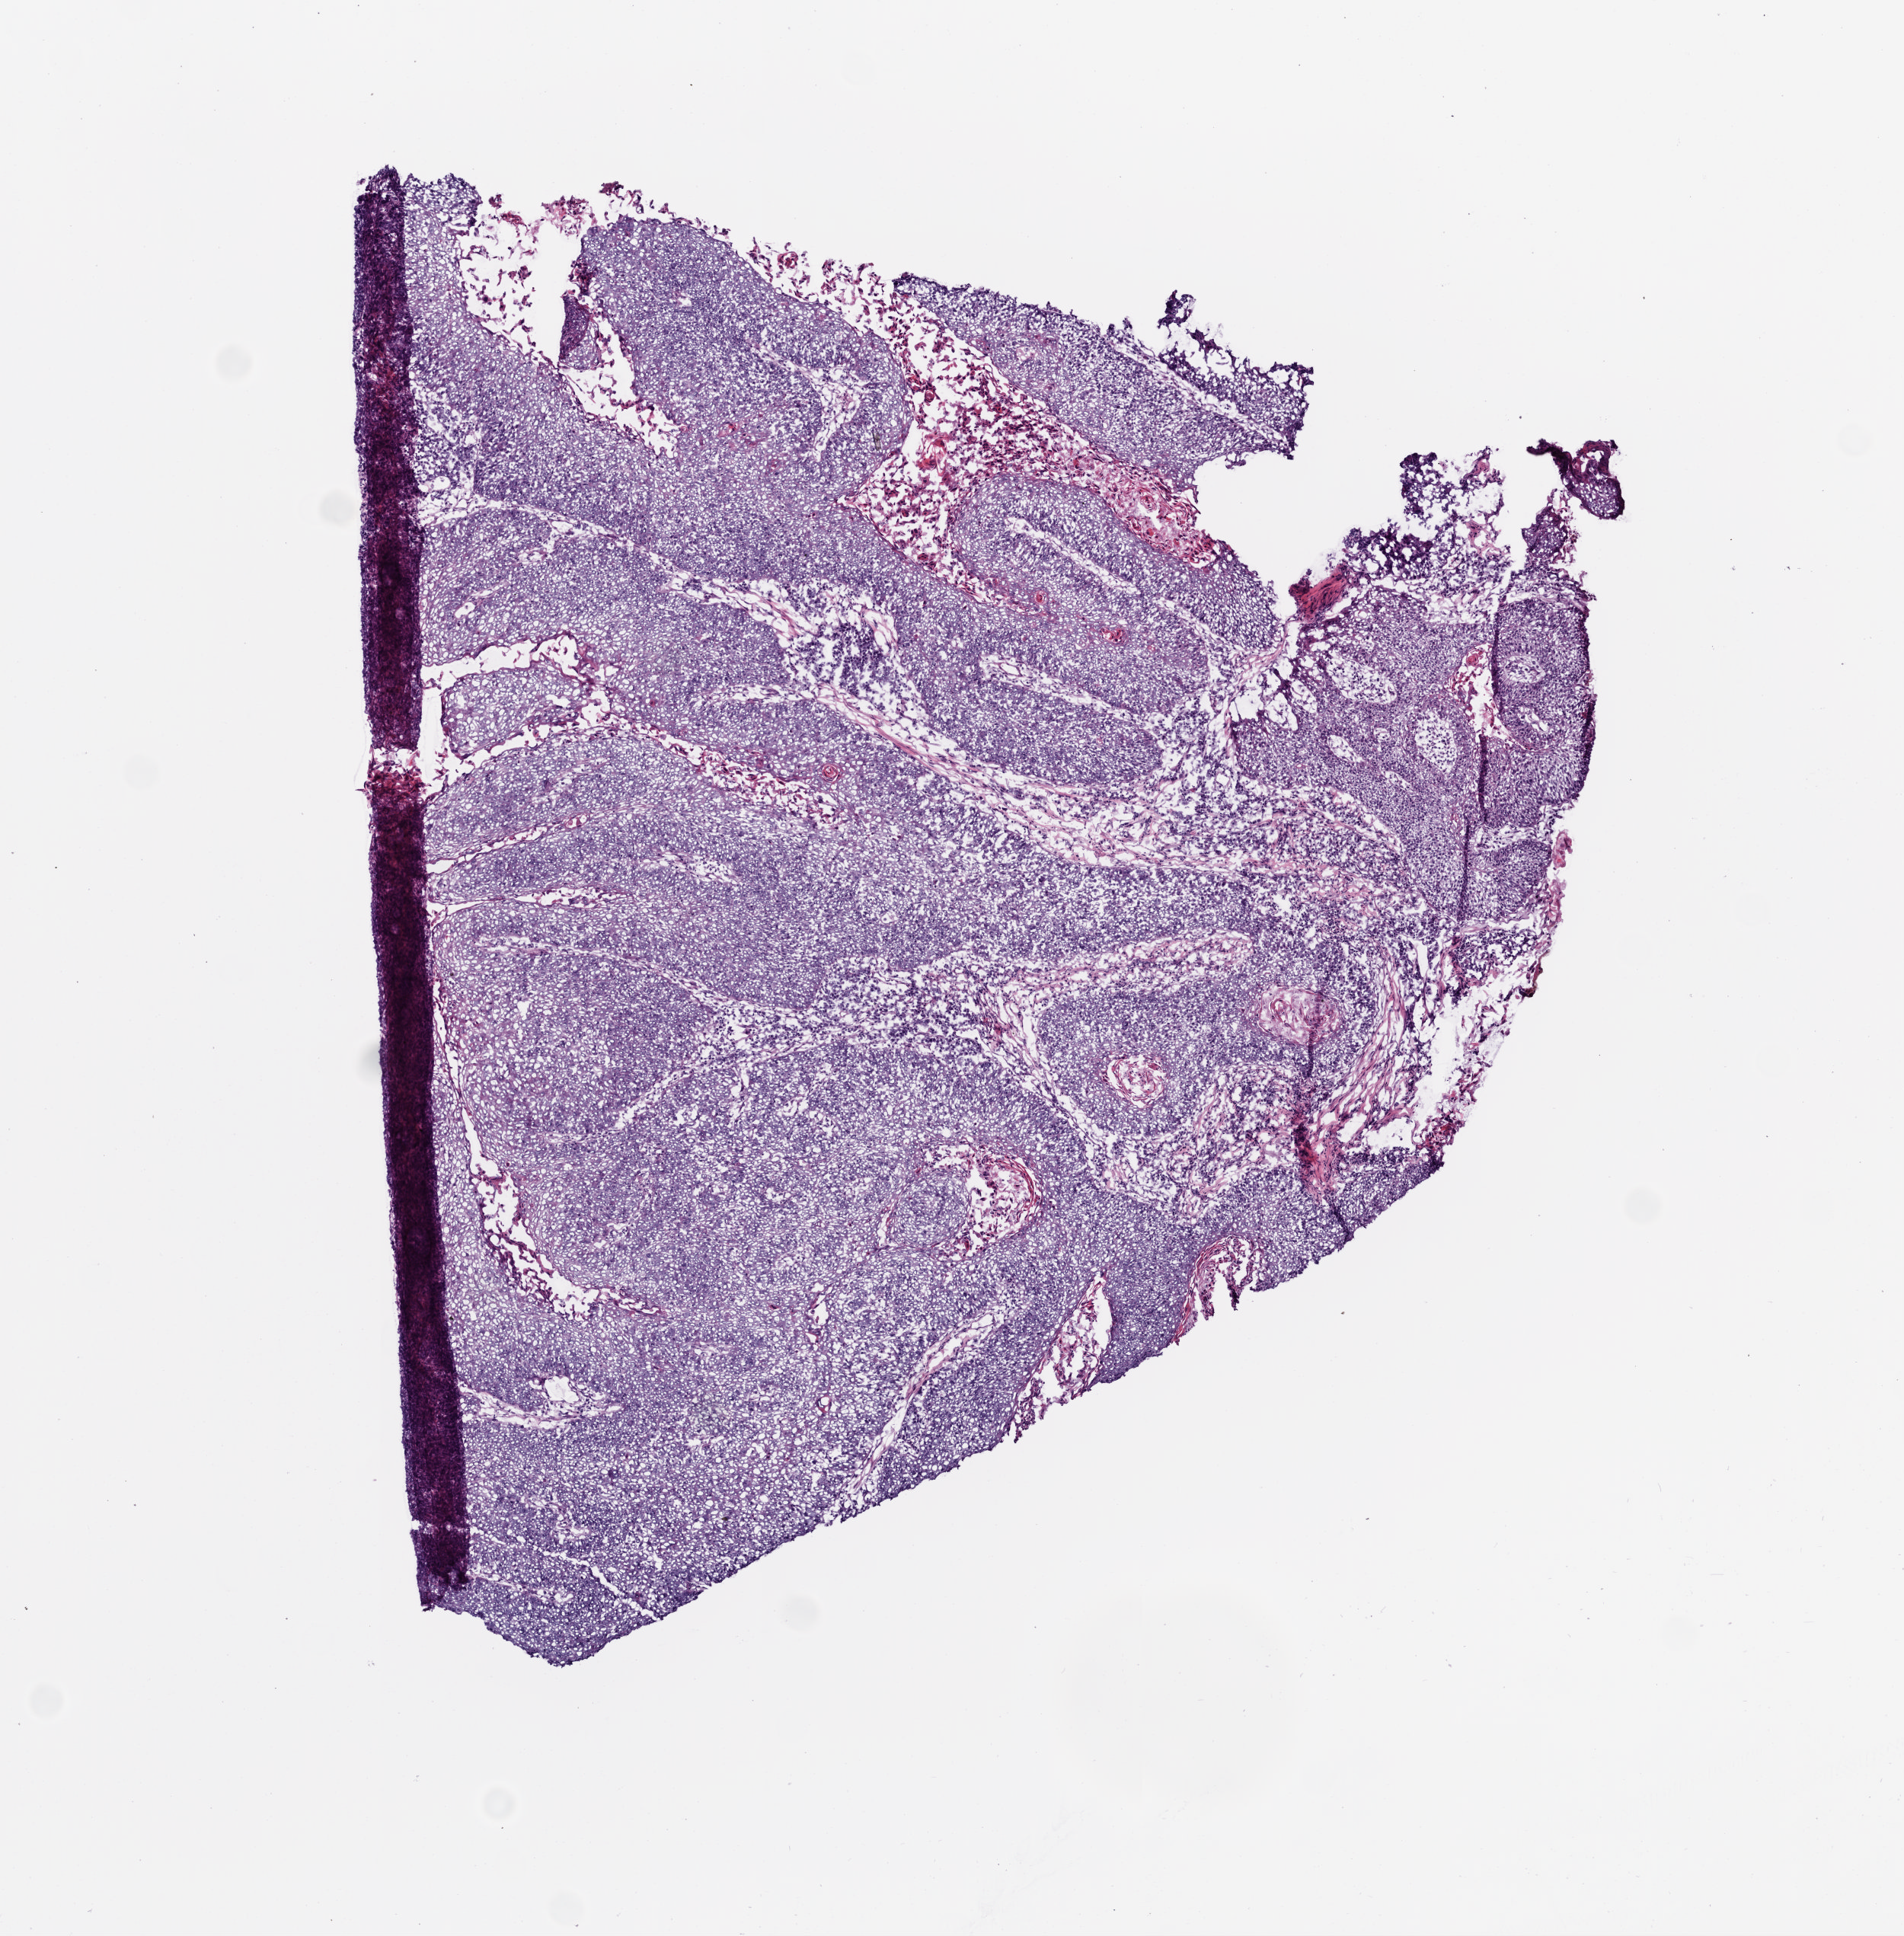
Whole-slide histology image, H&E, shown as a low-resolution overview of the whole scanned area (about 5.0 x 5.1 mm, from a 20x scan), frozen section, head and neck, primary tumour sample. Male patient; age at initial diagnosis 82 years. Pathologist review of this section (percent, as recorded): tumour cells 96%, tumour nuclei 80%.
Diagnosis: Squamous cell carcinoma, NOS (overlapping lesion of lip, oral cavity and pharynx).